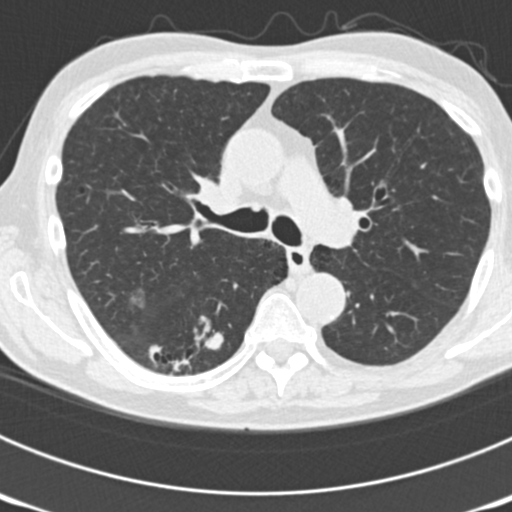
Low-dose screening chest CT, one axial slice. Position 117 of 177 along the scan axis. Reconstruction kernel B30f. Lung window (W 1500 / L -600 HU). 512 × 512 image matrix, field of view 300 × 300 mm.
Outlined on this slice (outlined manually by an expert reader):
- lesion 6 (nodule, lower lobe of right lung): bounding box [x1, y1, x2, y2] px = [205, 333, 224, 350]